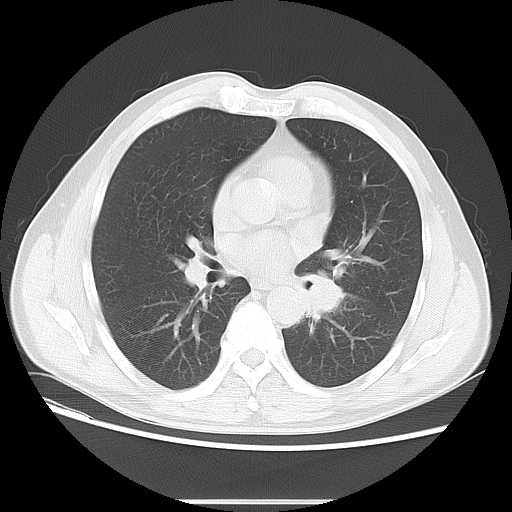
Chest CT, one axial slice. Position 29 of 59 along the scan axis. Reconstruction kernel LUNG. 120 kVp. Lung window (W 1500 / L -600 HU). 5 mm slice thickness. 512 × 512 image matrix, field of view 378 × 378 mm. Male patient, age 59 years. Case-level facts recorded for this patient, not image findings: clinical TNM (as recorded): T2 N3 M0; histopathological grade: G3.
Outlined on this slice (rectangle marked by the reading radiologist):
- lung tumour (recorded histology: small cell carcinoma): box from (x=302, y=268) to (x=354, y=327) px